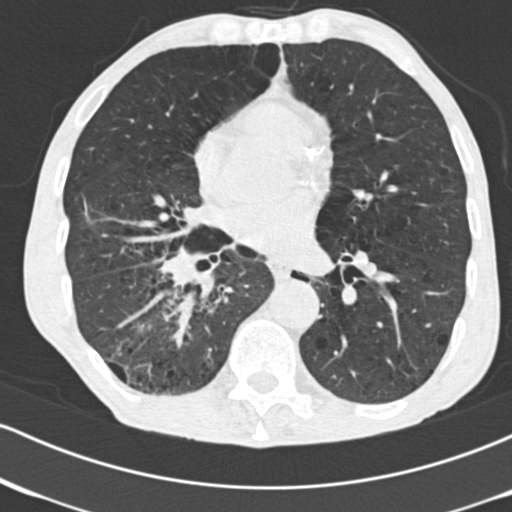
Low-dose screening chest CT, axial slice; second annual screen; lung window (W 1500 / L -600 HU); standard (soft-tissue) reconstruction kernel (B30f); 120 kVp. Male, age 64 years at enrolment. Current smoker at enrolment.
- Lesion marked by an expert reader, bounding box <124,225,242,338> (left, top, right, bottom; pixels).
- Screening reader's record for this exam (one nodule recorded; not confirmed to be the boxed lesion): non-calcified nodule or mass ≥4 mm, 52 × 37 mm, spiculated (stellate) margins, soft tissue attenuation, pre-existing on the prior screen: no.
- Later outcome: lung cancer diagnosed 28 days after this screen — adenocarcinoma, NOS, right lower lobe, stage IV (AJCC 6th edition), 60 mm at pathology.